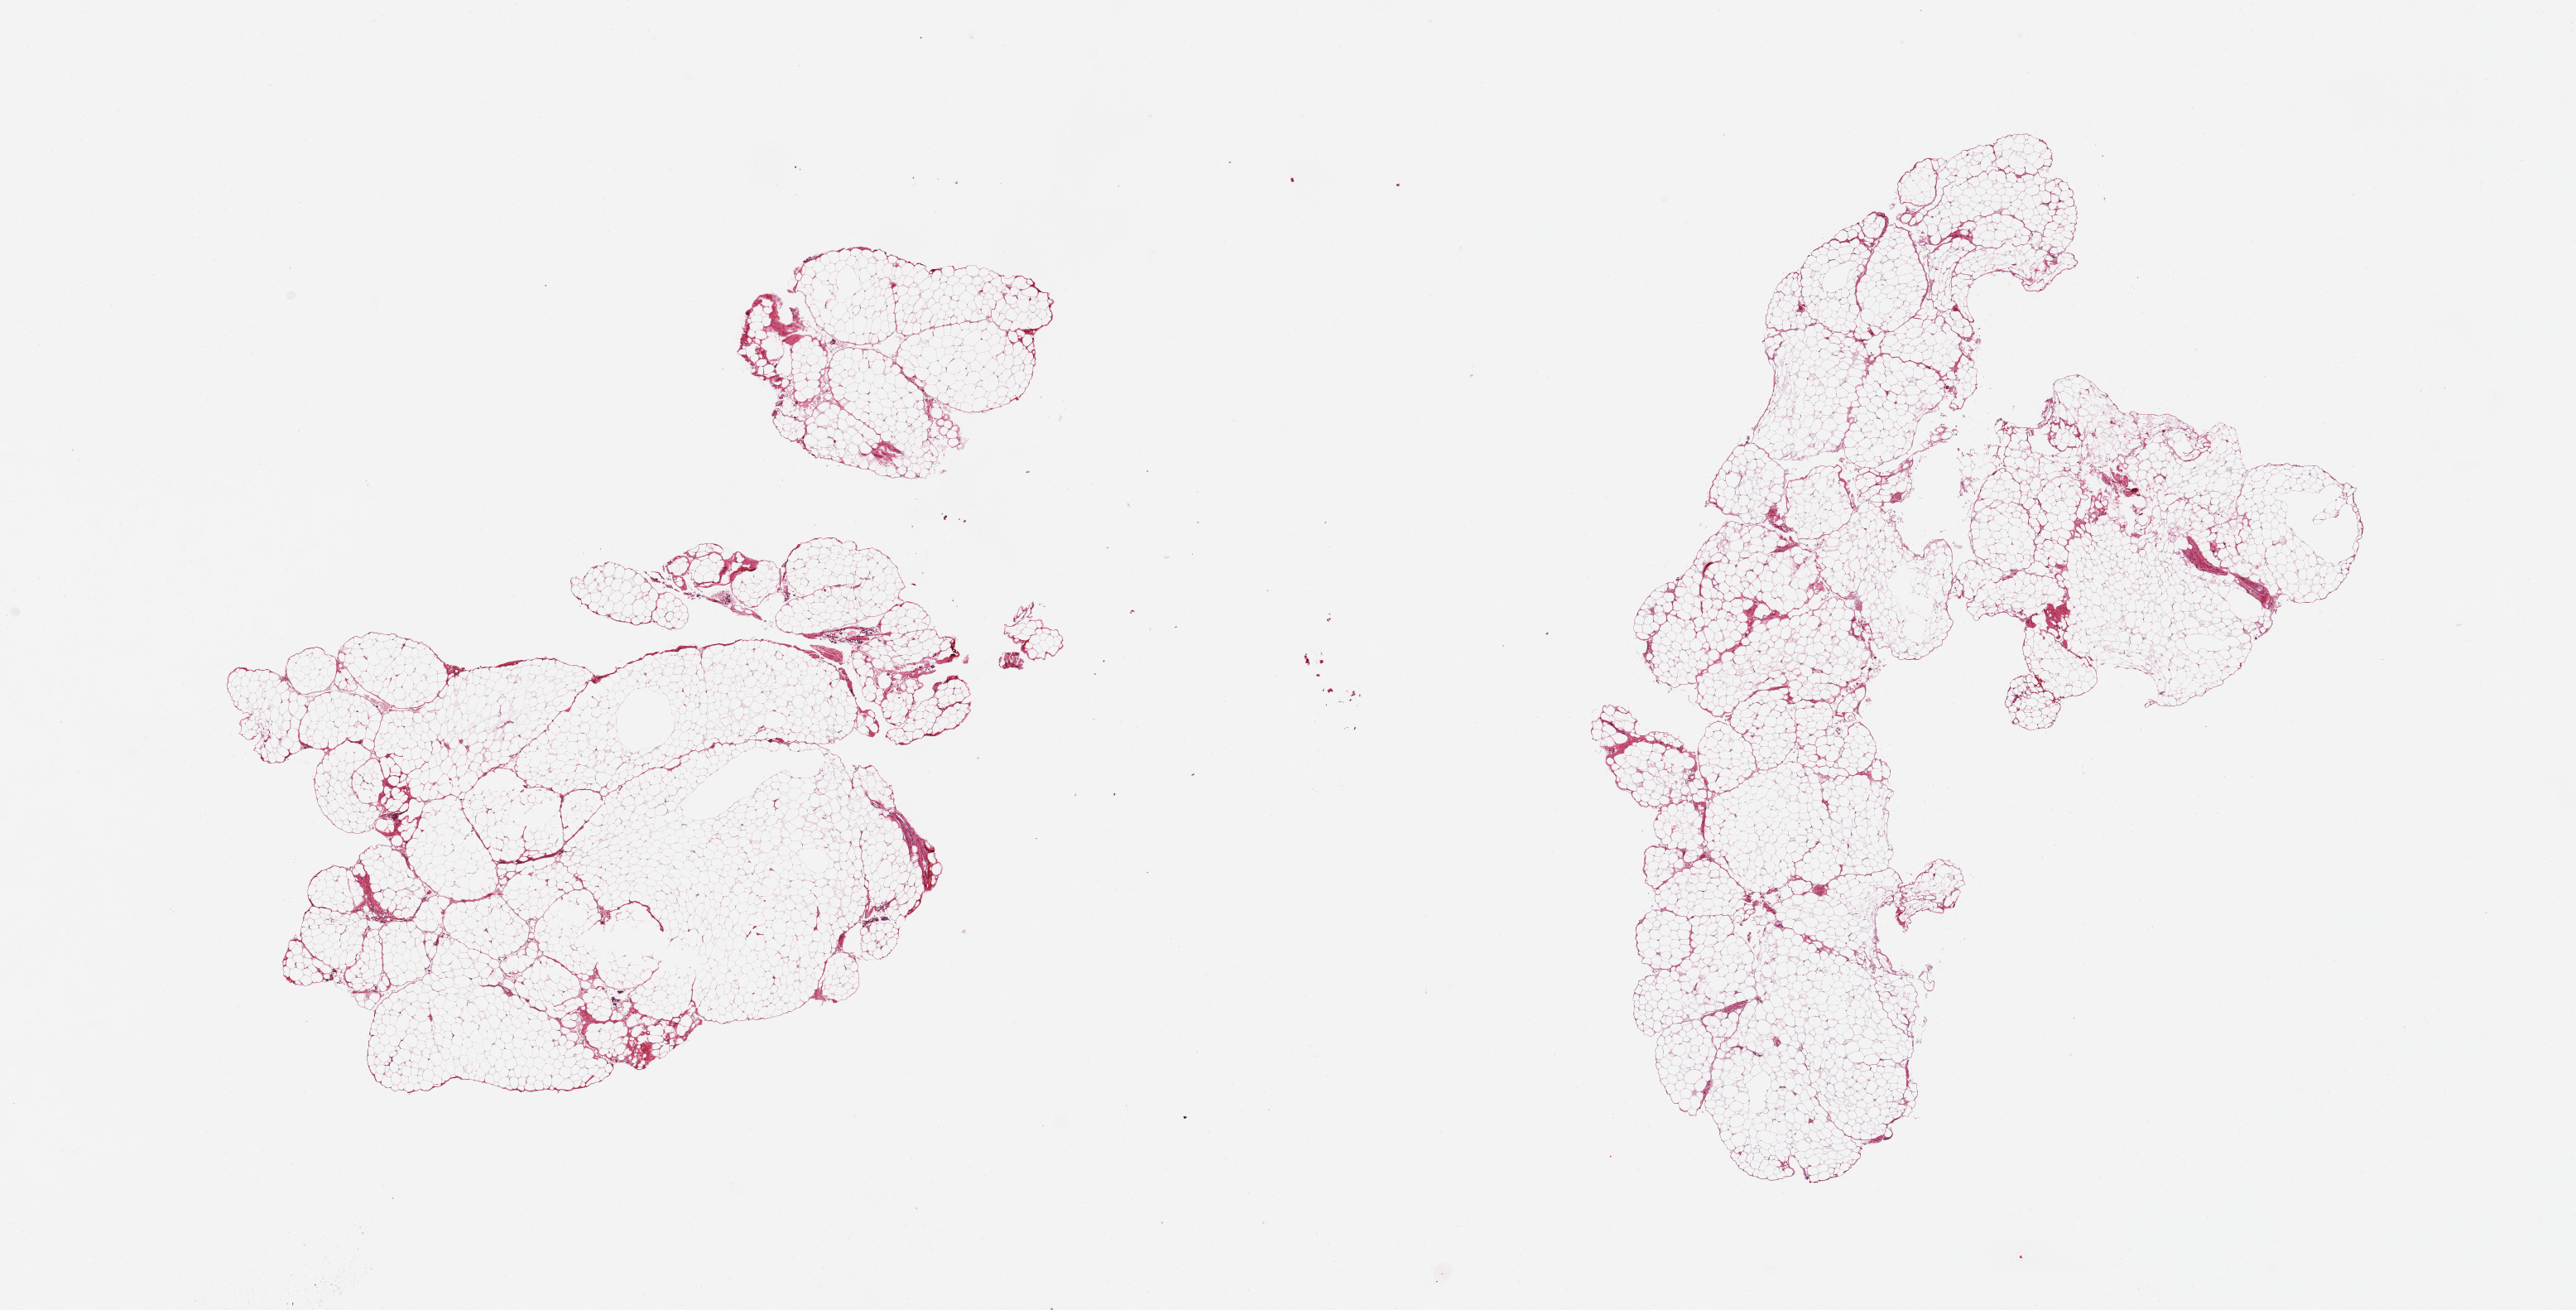
Digitized hematoxylin and eosin (H&E)-stained section, brightfield — shown as a low-resolution overview of the whole scanned area (about 24.6 x 12.5 mm, from a 20x scan); PAXgene-fixed, paraffin-embedded tissue; target tissue: omentum; donor tissue sample.
Reviewer comment on this tissue sample: 2 pieces; lobulated fat.